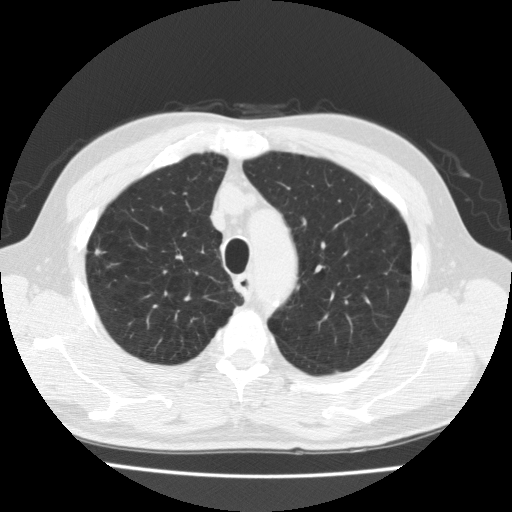
Low-dose screening chest CT, one axial slice; position 168 of 205 along the scan axis; reconstruction kernel FC10; 120 kVp; lung window (W 1500 / L -600 HU); 512 × 512 image matrix, field of view 350 × 350 mm.
Annotated regions visible in this slice (expert manual segmentation):
- lesion 1 (tumor, upper lobe of right lung): box from (x=95, y=247) to (x=106, y=255) px